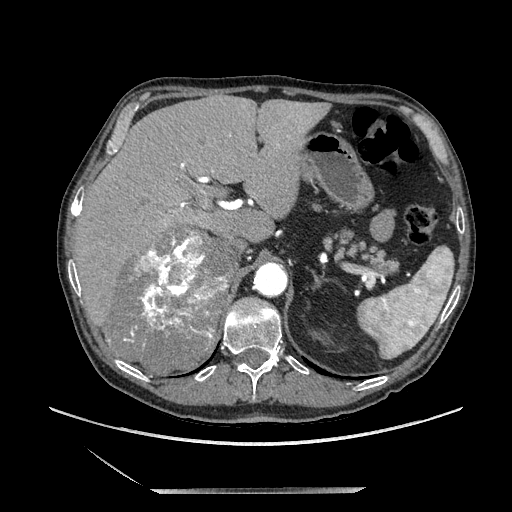
Contrast-enhanced abdominal CT, one axial slice; position 147 of 243 along the scan axis; soft-tissue window (W 400 / L 40 HU); 512 × 512 image matrix, field of view 420 × 420 mm. Male patient. From the clinical record (not read from this slice): diagnosis: adrenocortical carcinoma; tumour side: right adrenal; tumour size at pathology: 16 cm; Ki-67 index: 17 %; stage (as recorded): 3.
Outlined on this slice (semi-automatic segmentation, software-assisted and operator-edited):
- mass: bounding box (x1, y1, x2, y2) in pixels: (111, 229, 235, 374)